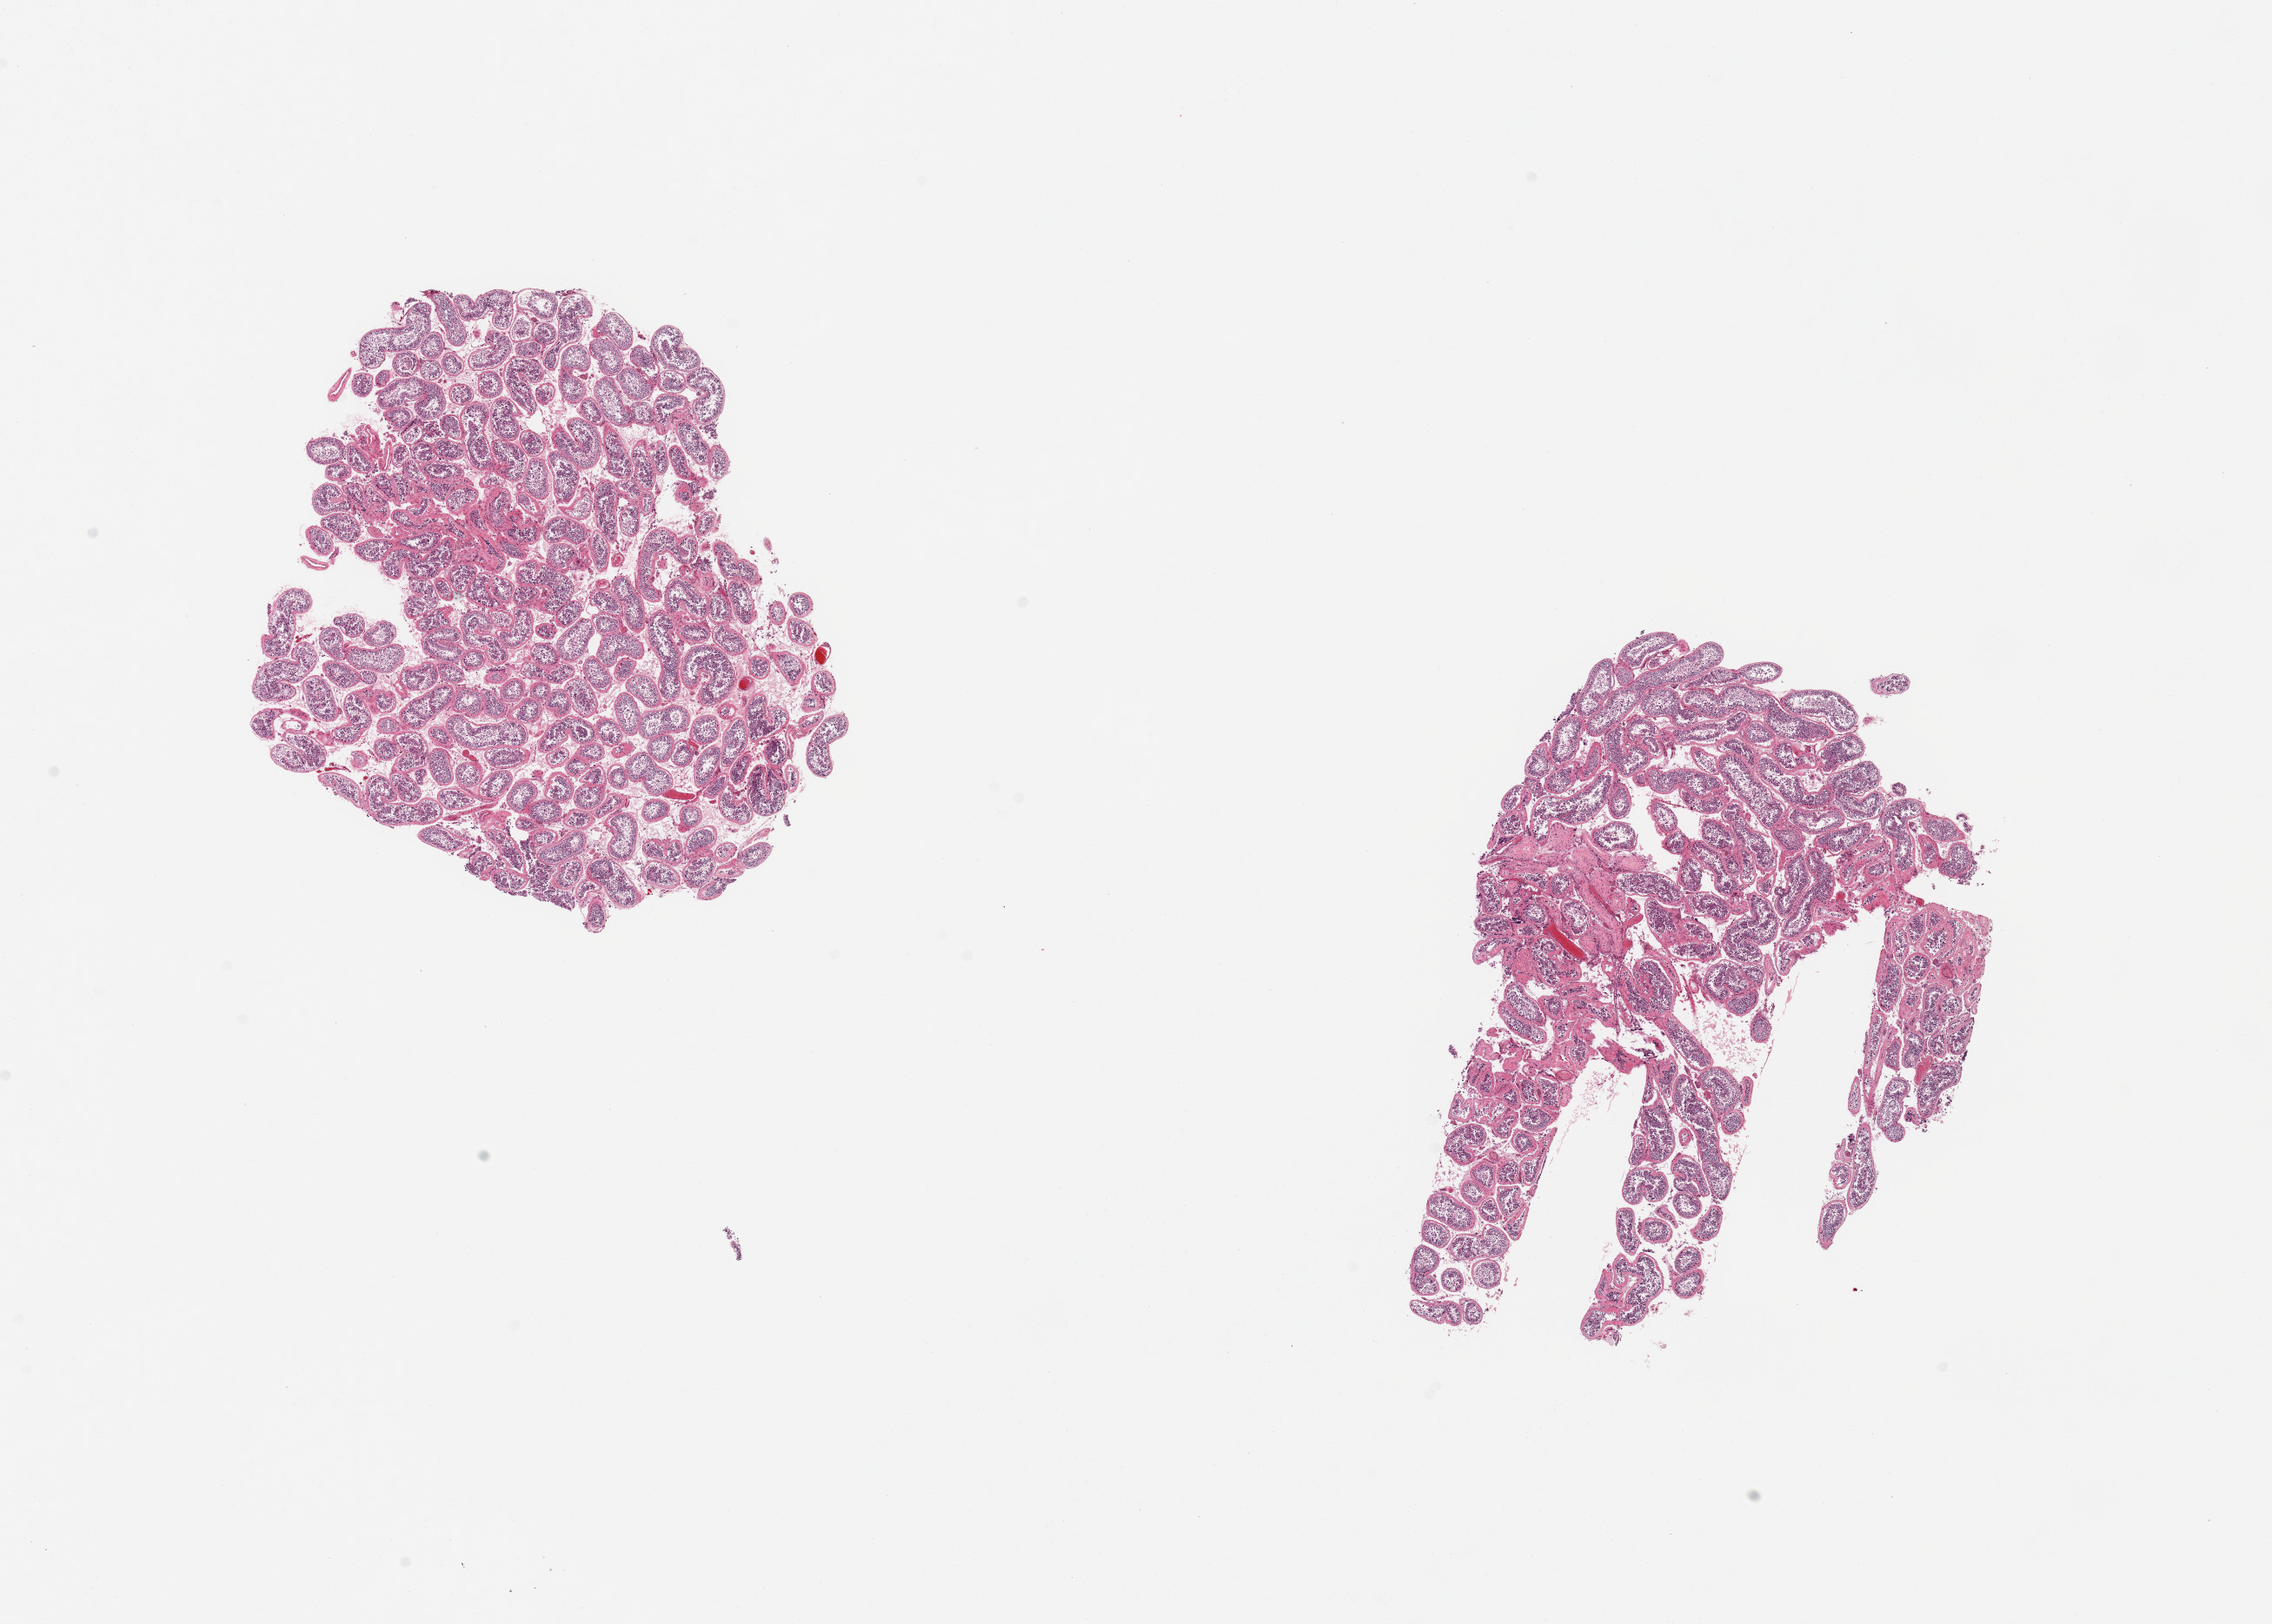
Hematoxylin and eosin (H&E) whole-slide image, brightfield, shown as a low-resolution overview of the whole scanned area (about 20.7 x 14.8 mm), PAXgene-fixed, paraffin-embedded tissue, section of testis (target tissue), donor tissue sample. Donor: male.
Reviewer comment on this tissue sample: 2 pieces; spermatogenesis present; focal fibrosis and sclerosis of tubules.